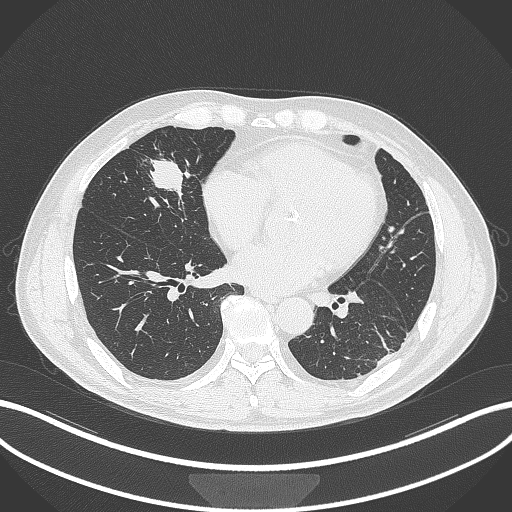
Chest CT, one axial slice; slice 111 of 399 in the series (ordered by position); reconstruction kernel B70f; 120 kVp; lung window (W 1500 / L -600 HU); 512 × 512 image matrix. Patient: male, 59 years. Case-level facts recorded for this patient, not image findings: clinical TNM (as recorded): T2a N1 M0.
Structures marked on this image (bounding box drawn by a radiologist):
- lung tumour (recorded histology: adenocarcinoma): box from (x=144, y=157) to (x=190, y=198) px